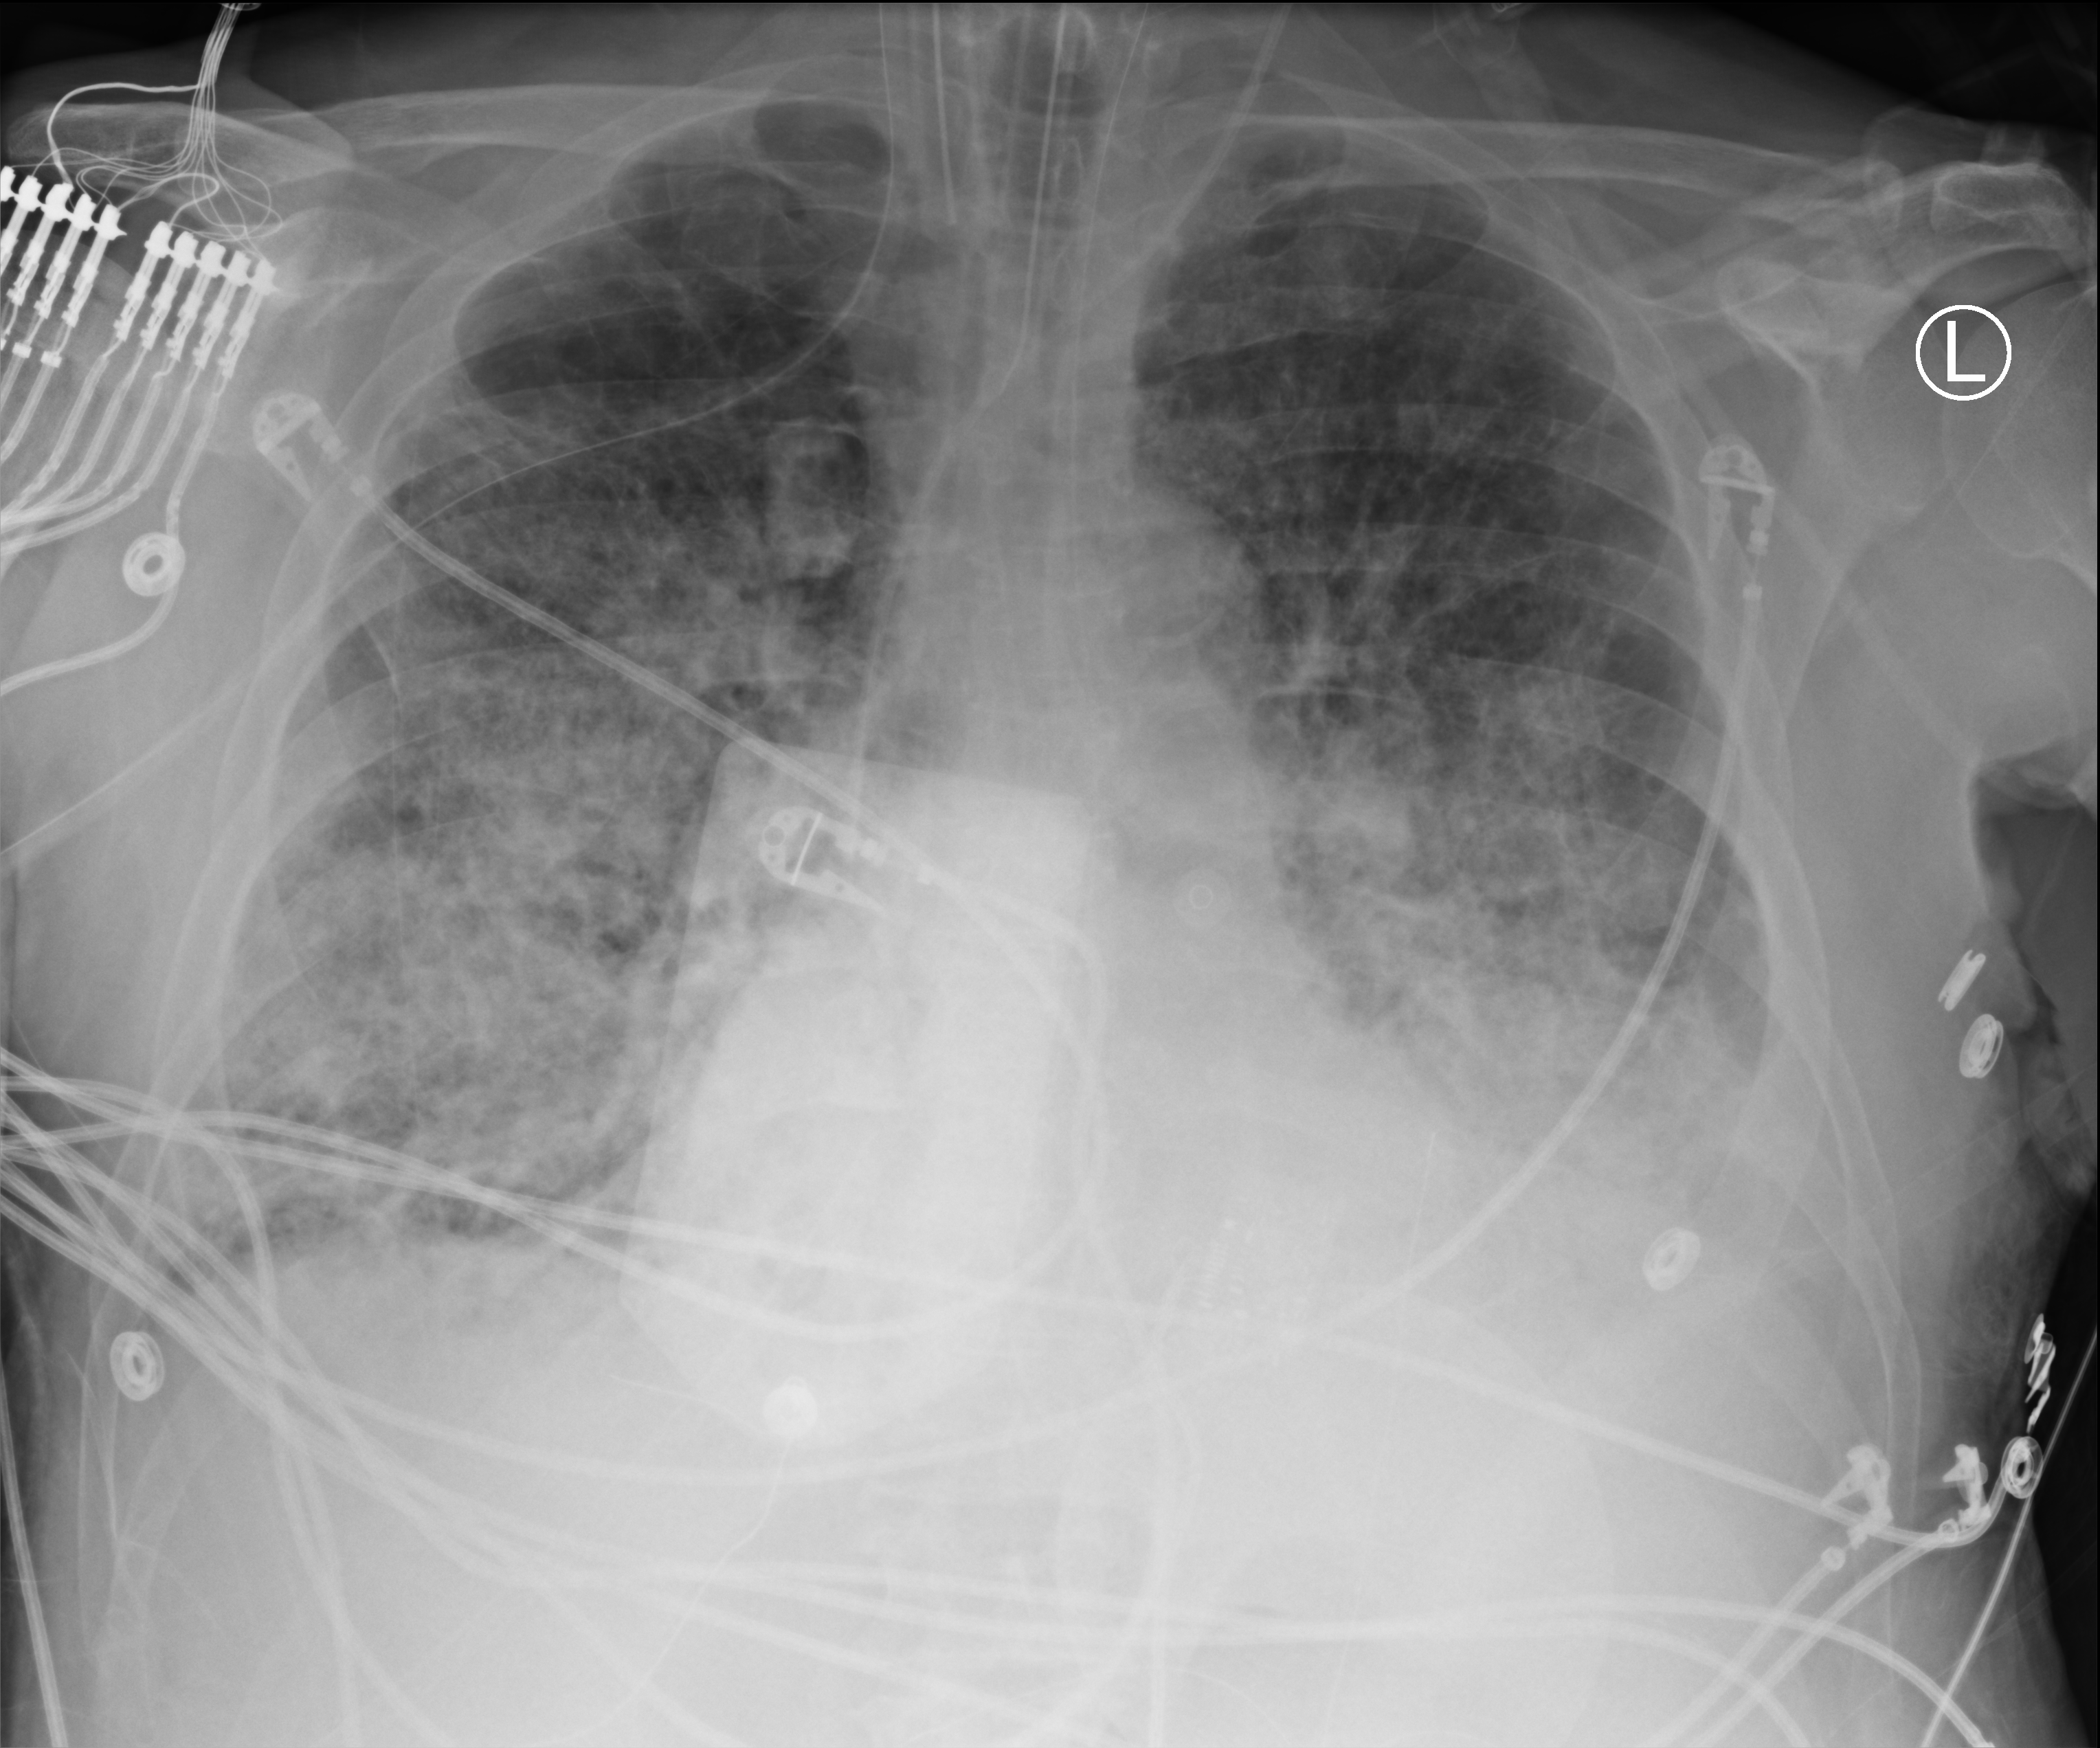
Bedside chest radiograph (computed radiography), anteroposterior (AP) projection. Patient hospitalised with COVID-19; male, aged 75–90 years.
From the hospital-stay record, not from the radiograph (when in the stay this image was taken is not recorded):
- admitted to intensive care during this hospital stay: yes
- mechanically ventilated during this hospital stay: yes
- chronic kidney disease (admission record): no